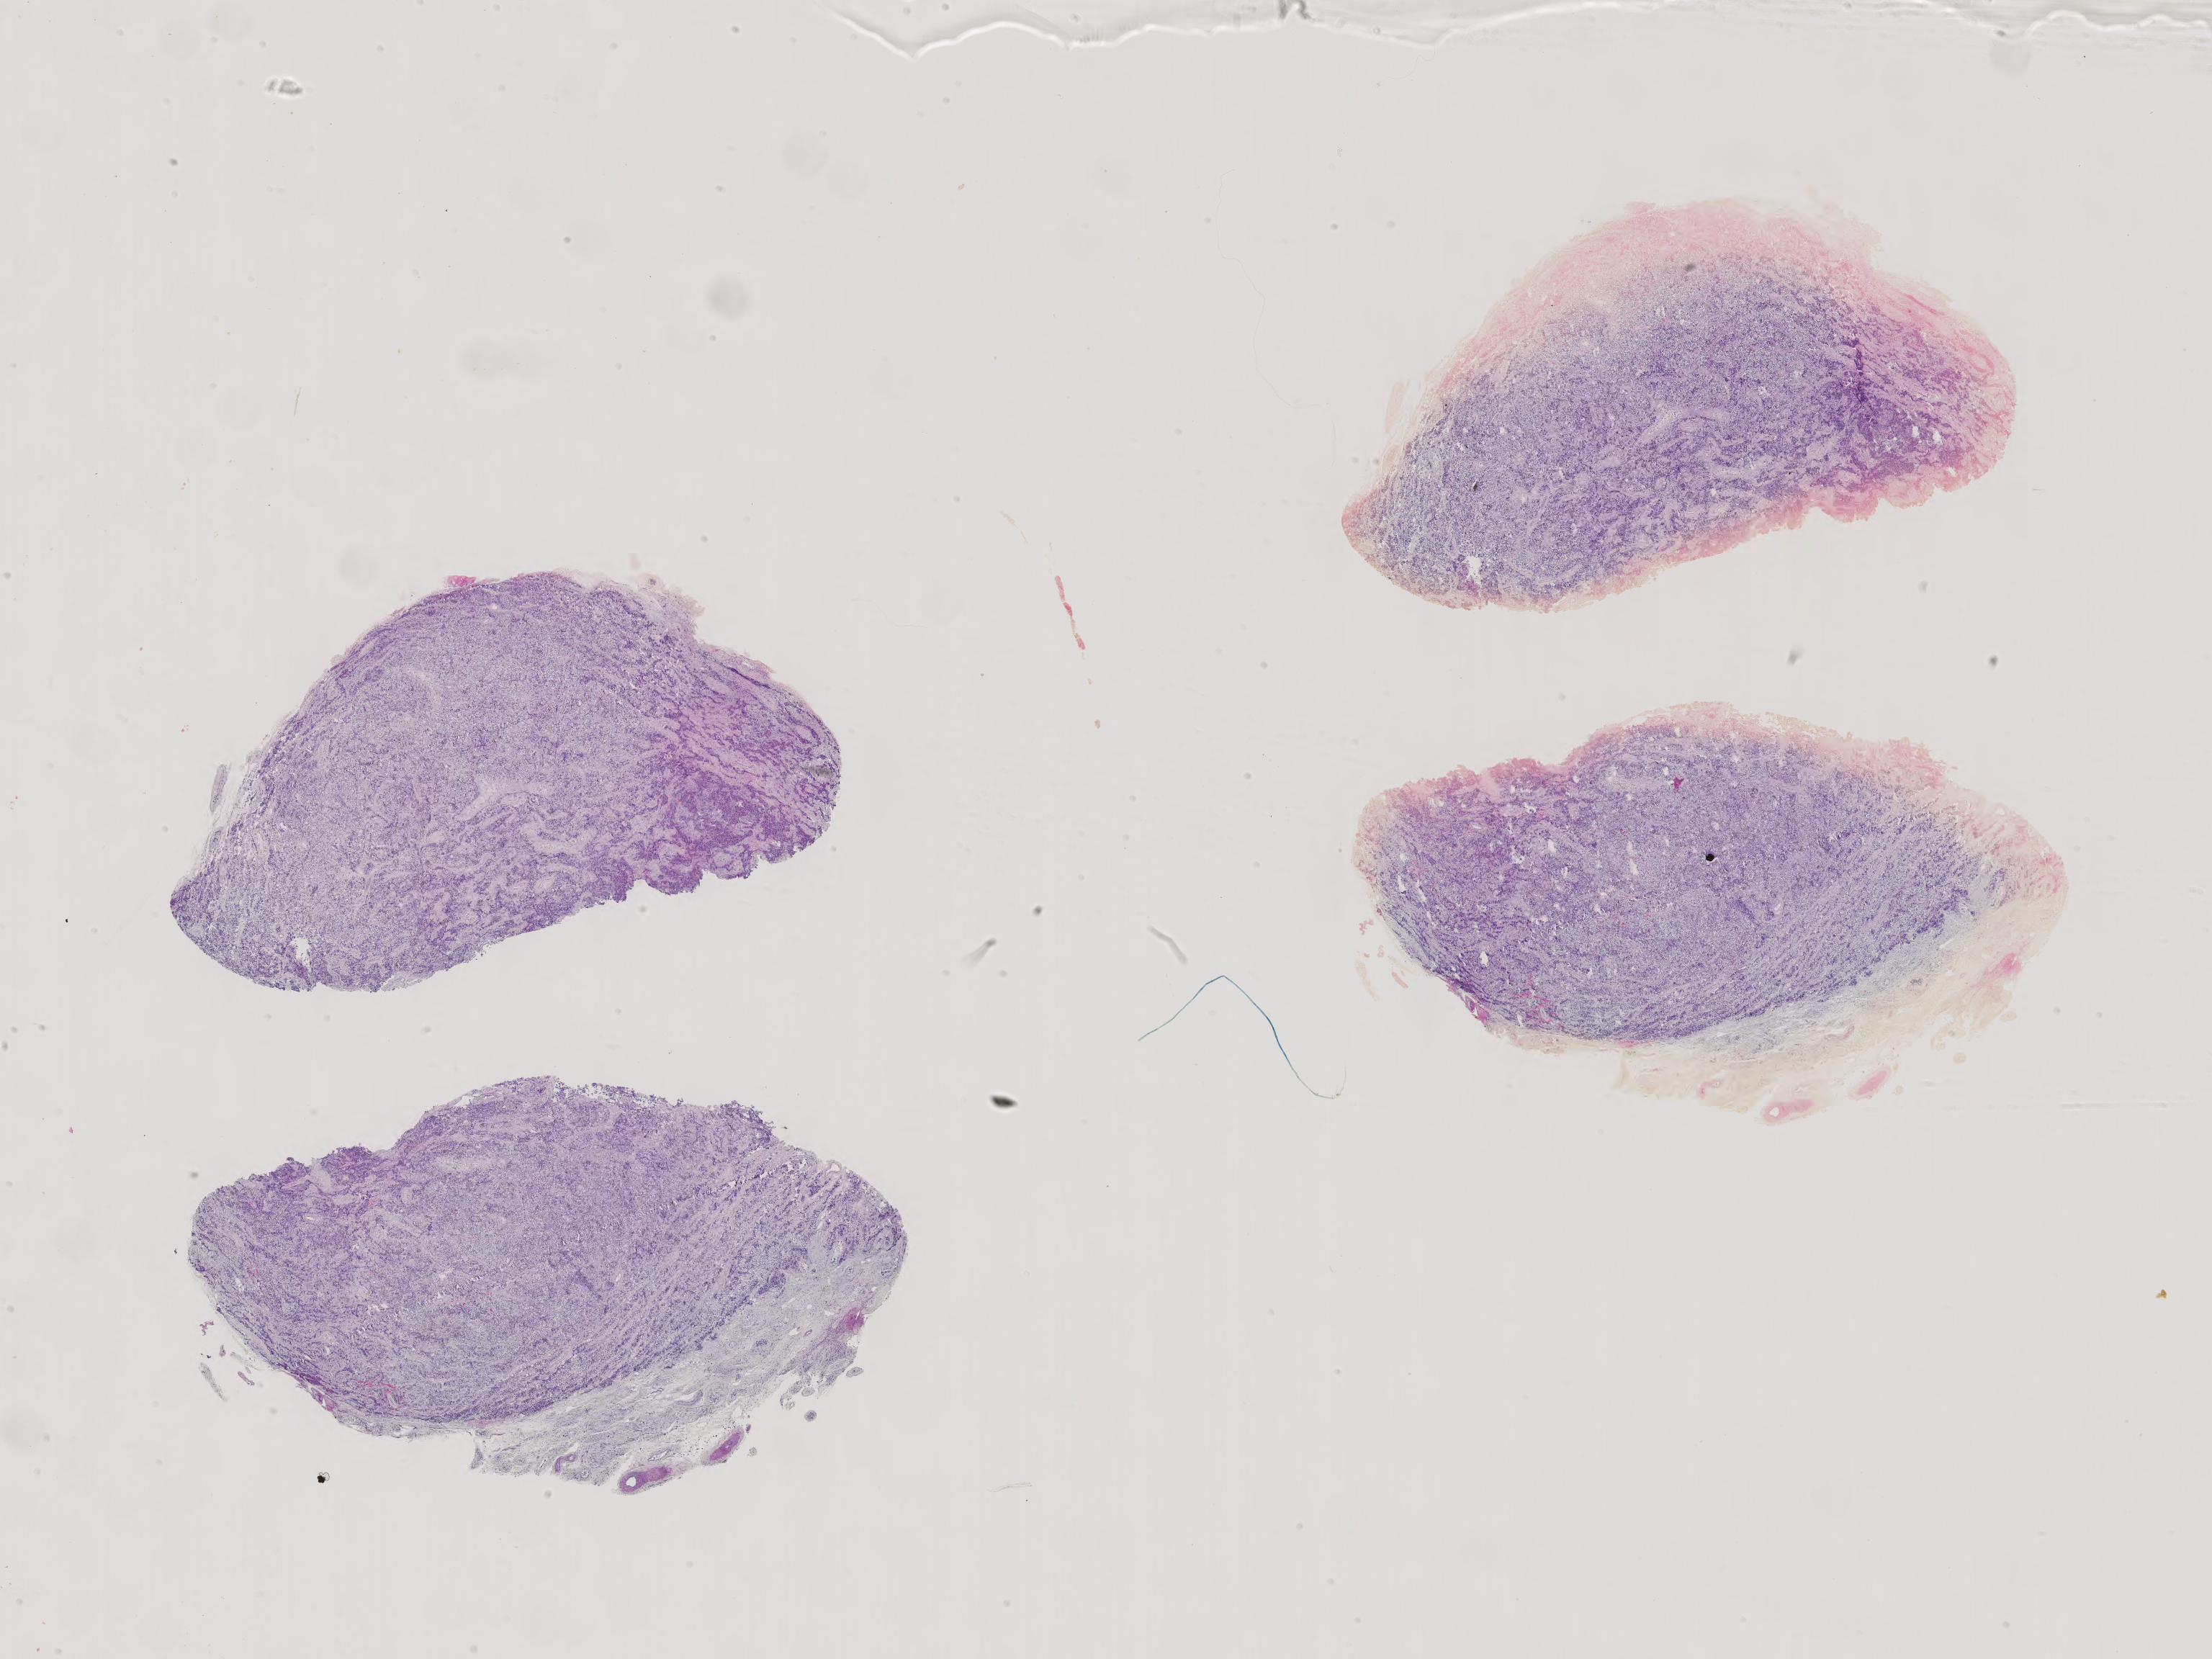
Whole-slide histology image, H&E-stained, low-resolution overview of the scanned area, about 22.4 x 16.8 mm (acquisition: 40x scan); FFPE section; sample: primary tumour, testis. Male patient; age at initial diagnosis 25 years.
• diagnosis: Seminoma, NOS
• AJCC pathologic stage: I
• TNM: T1 N0 M0
• laterality: left